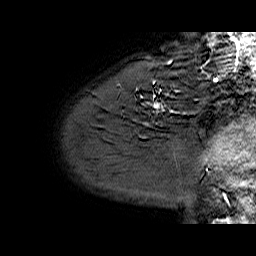
Breast MRI (dynamic contrast-enhanced), one sagittal slice; slice 51 of 60 in the series (ordered by position); dynamic contrast-enhanced series, time point 2 of 6 at this slice position (early post-contrast); 1.5 T; TE 6.4 ms, TR 32.9 ms; 4 mm slice thickness; 256 × 256 image matrix, field of view 200 × 200 mm. Female patient. From the clinical record (not read from this slice): setting: breast cancer imaged before/during neoadjuvant chemotherapy; receptor status: HER2-positive.
Outlined on this slice (semi-automatic segmentation, software-assisted and operator-edited):
- analysis volume of interest (the breast-tissue region the enhancement analysis was run in; not a lesion): bounding box (x1, y1, x2, y2) in pixels: (130, 62, 209, 128)
- tumour enhancement mask (voxels above the 100 % enhancement threshold inside the analysis volume of interest): (153, 62, 170, 107)